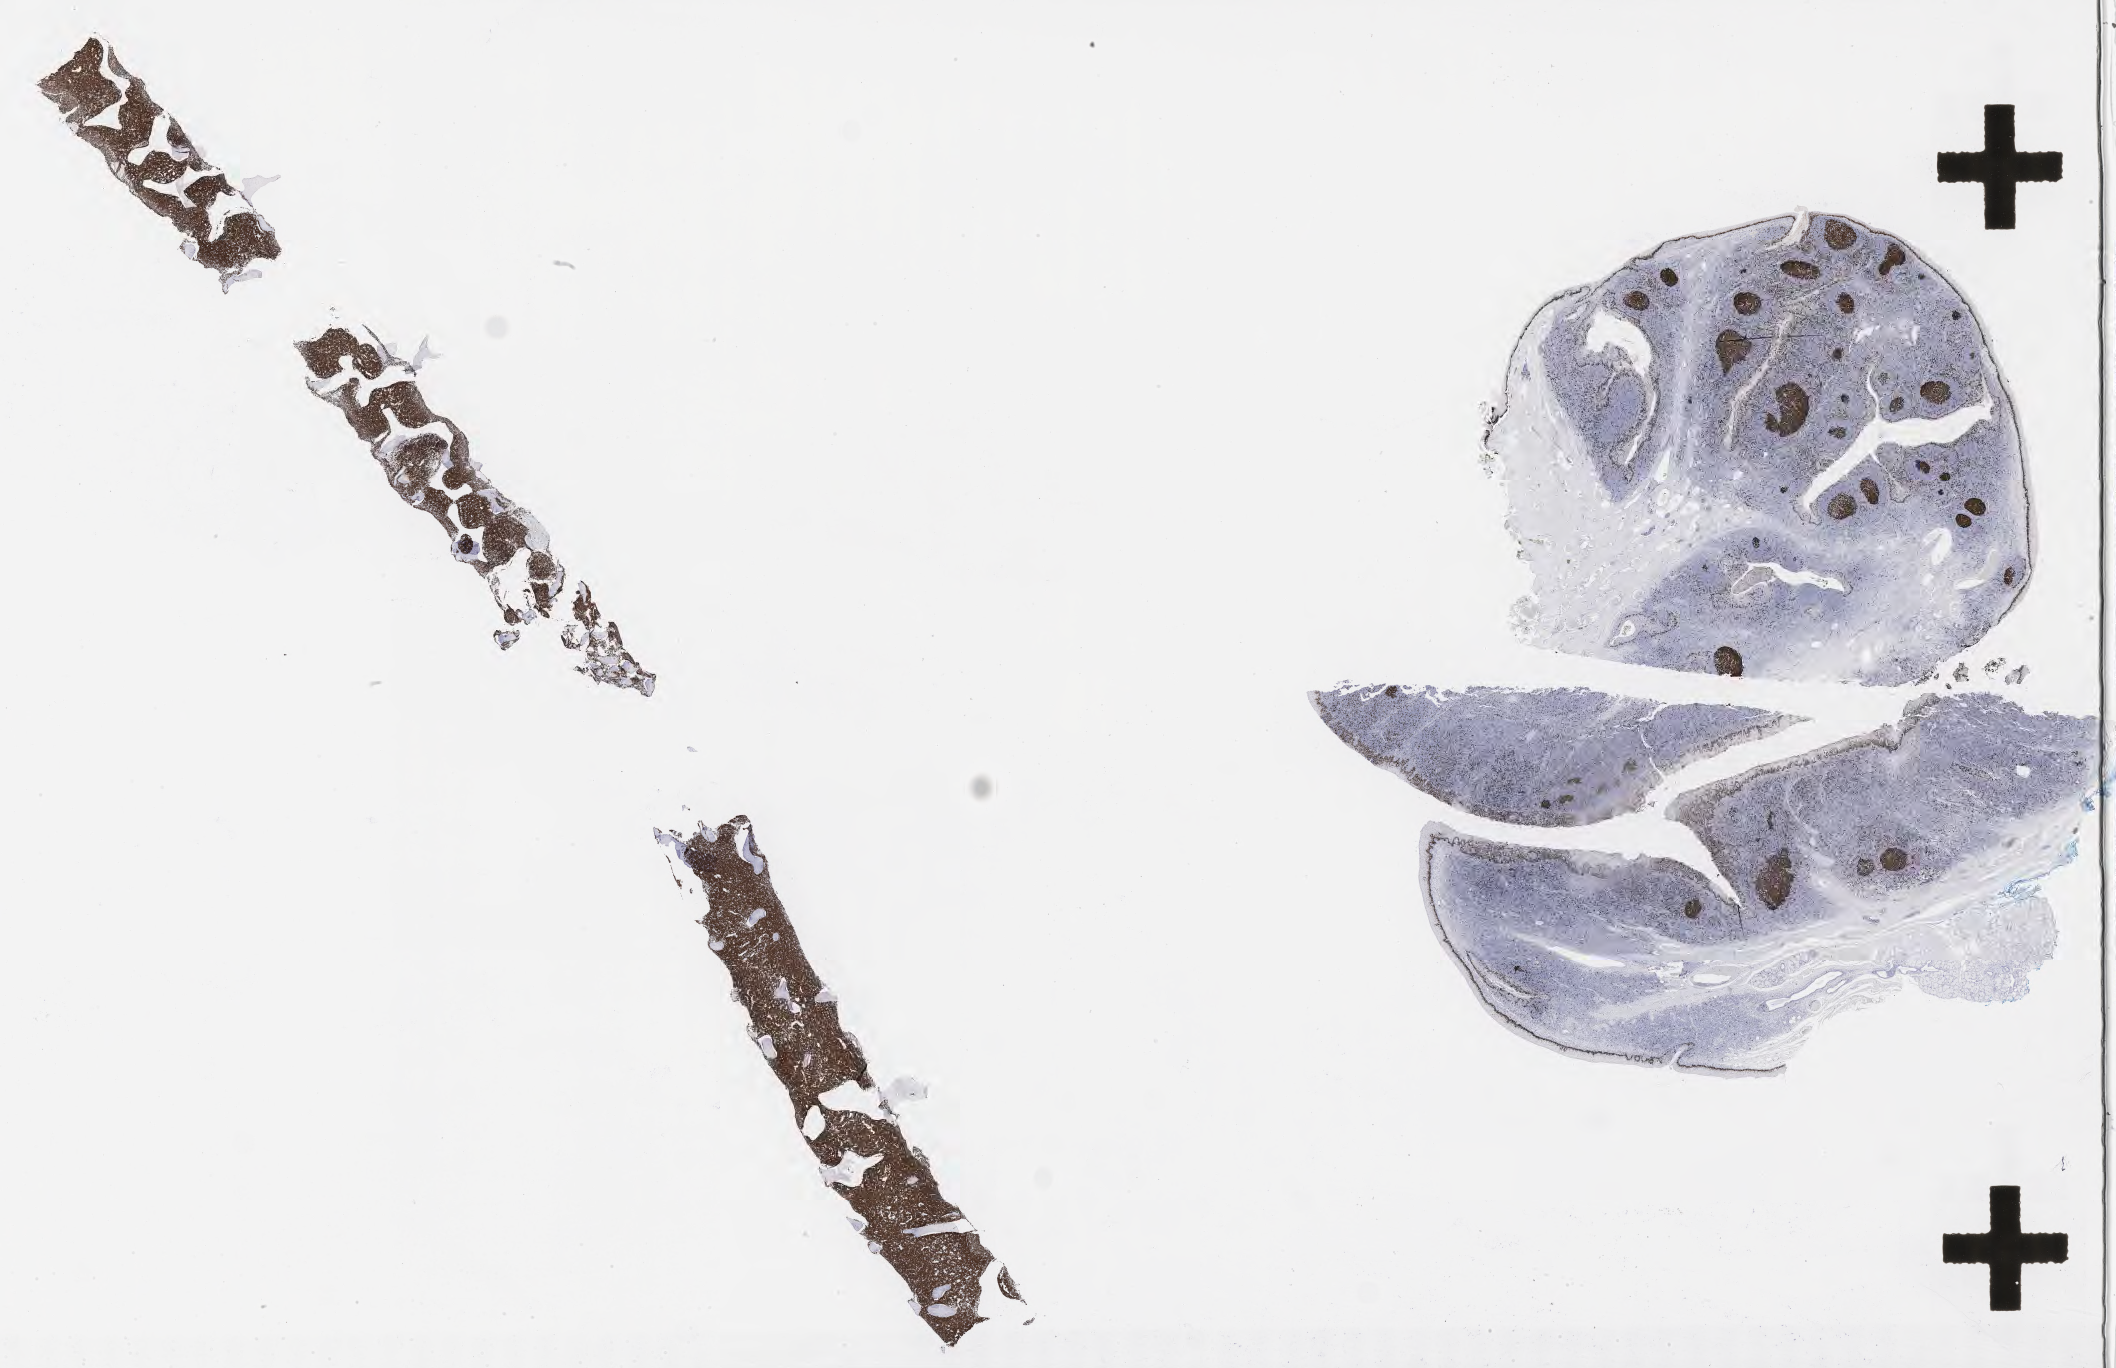
IHC for Ki-67, whole-slide image — low-resolution overview of the scanned area, about 34.2 x 22.1 mm; tumor tissue. Male patient; age at initial diagnosis 7 years.
Diagnosis: Burkitt lymphoma, NOS.